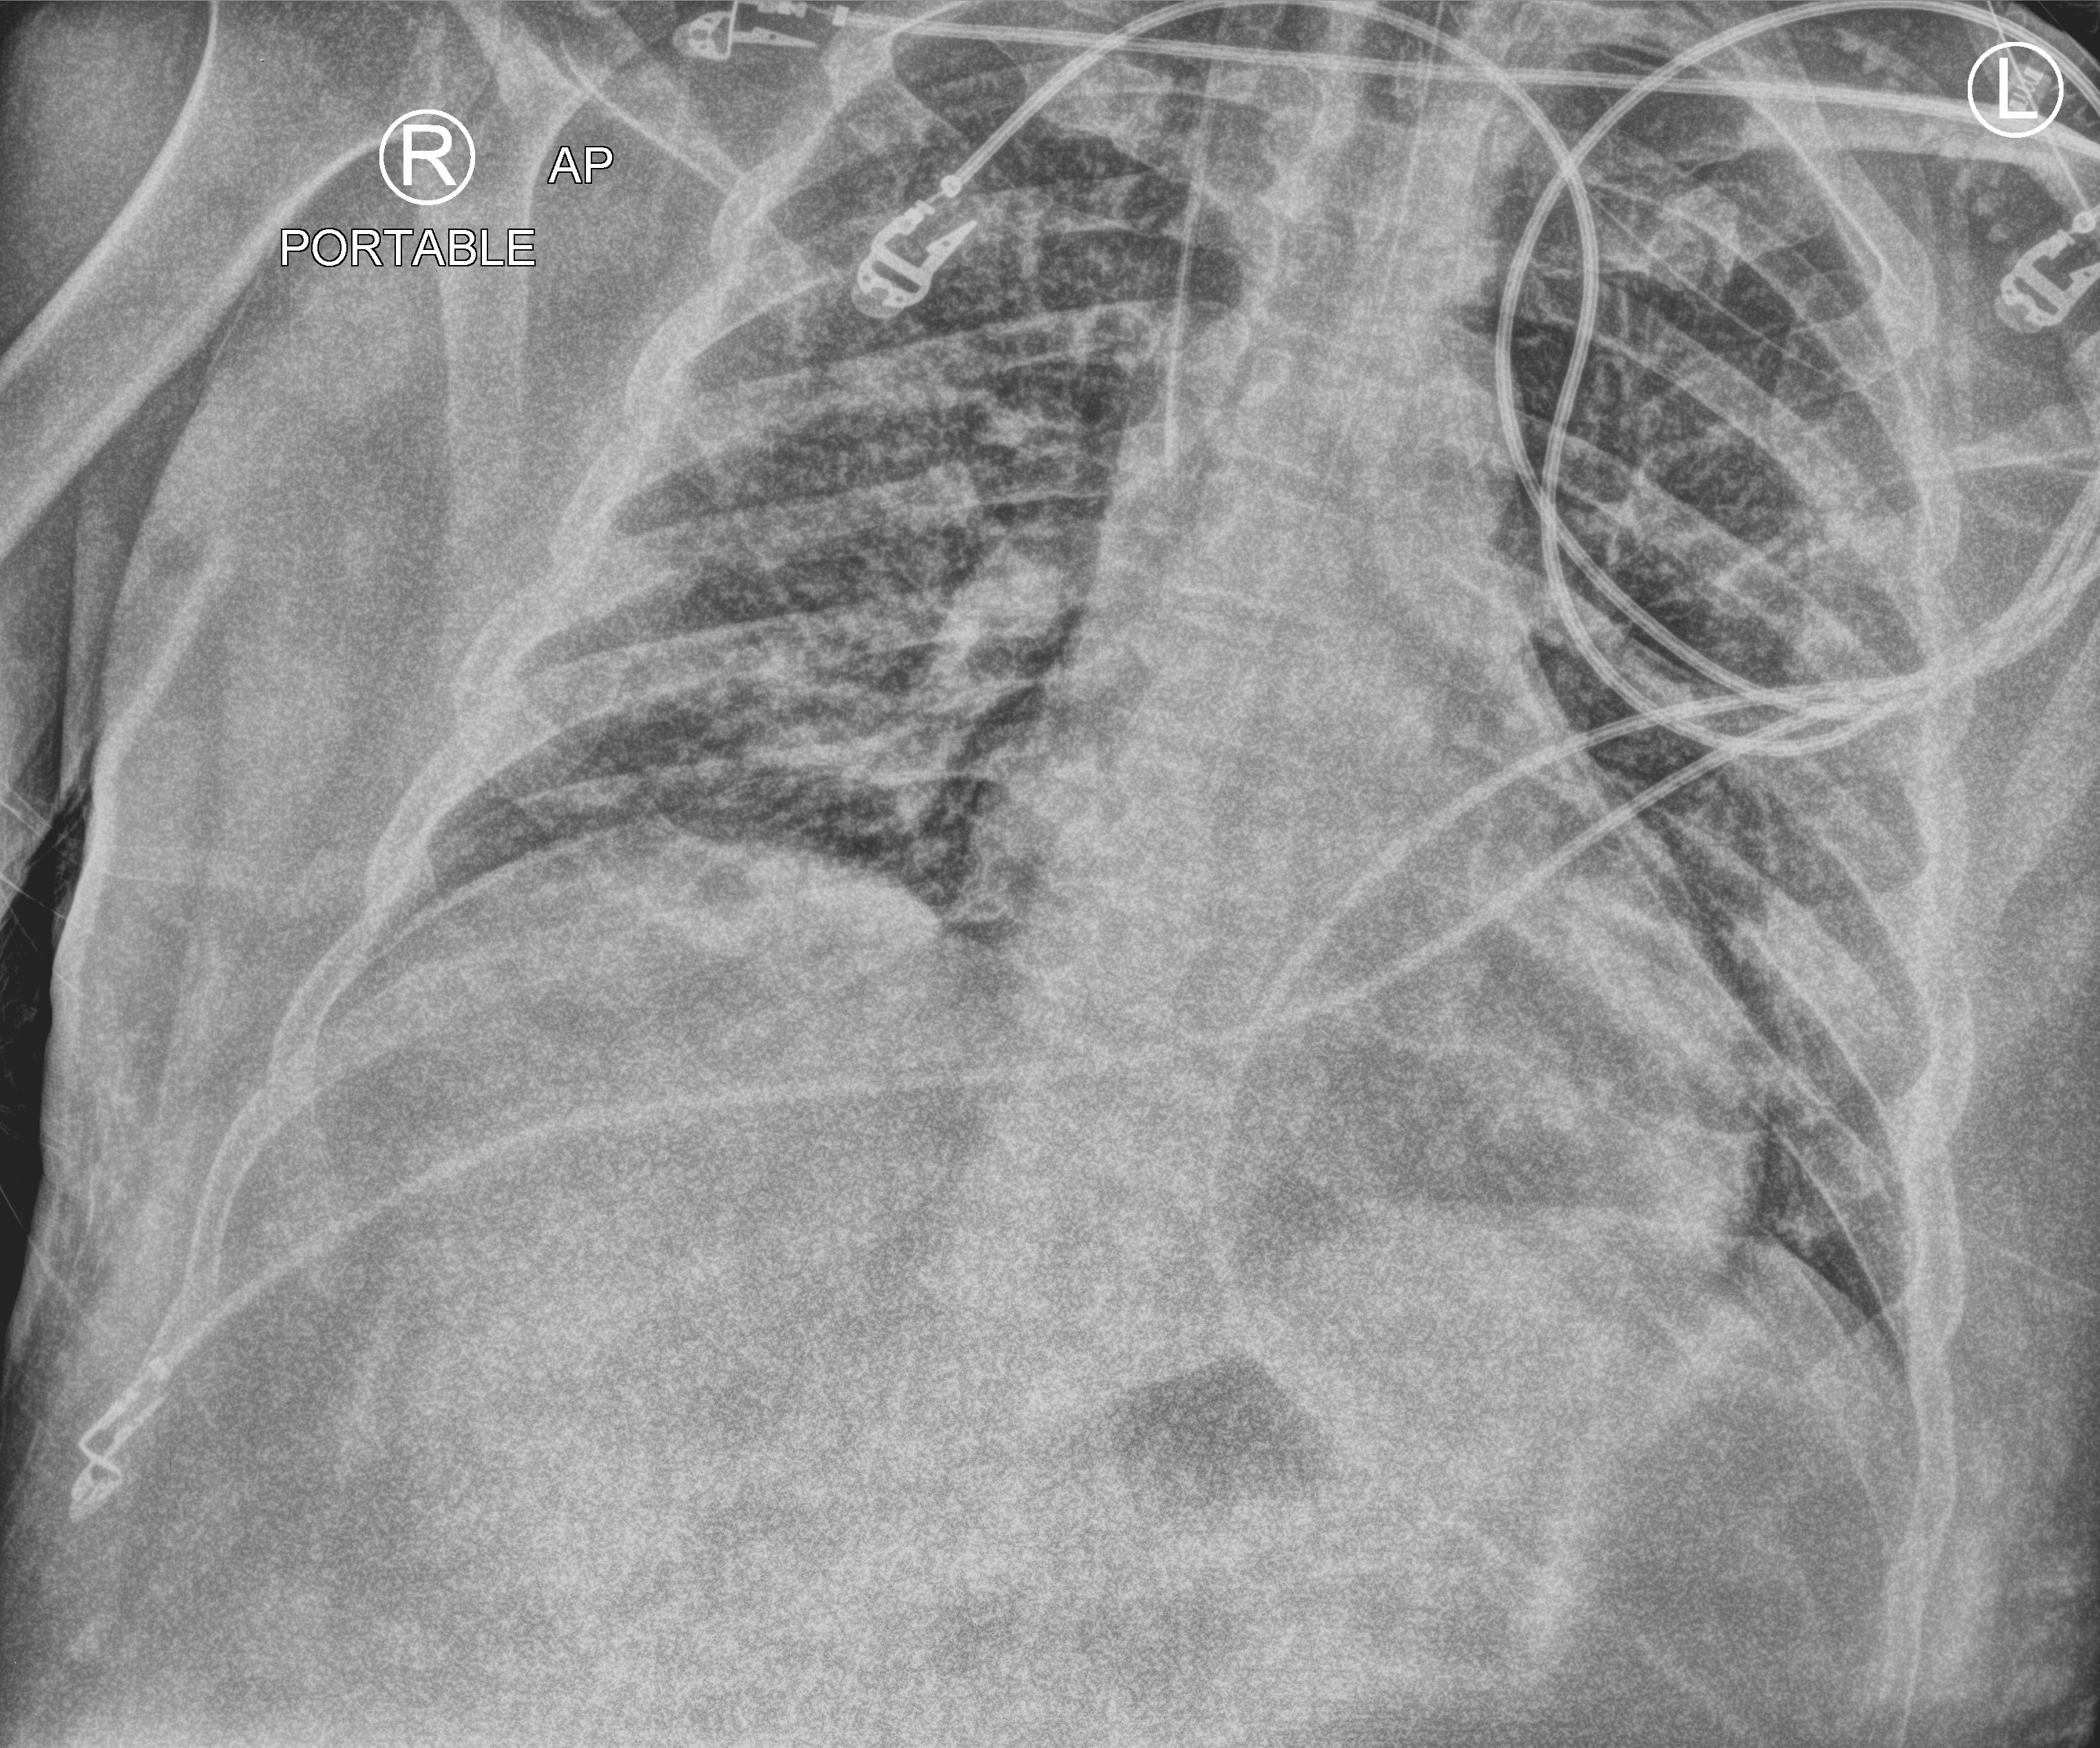
Bedside chest radiograph (computed radiography), anteroposterior (AP) projection. Patient hospitalised with COVID-19; male, aged 18–59 years.
Admission-level facts for this patient (not findings on this image; timing relative to this image not recorded): length of hospital stay: 32 days; admitted to intensive care during this hospital stay: no.